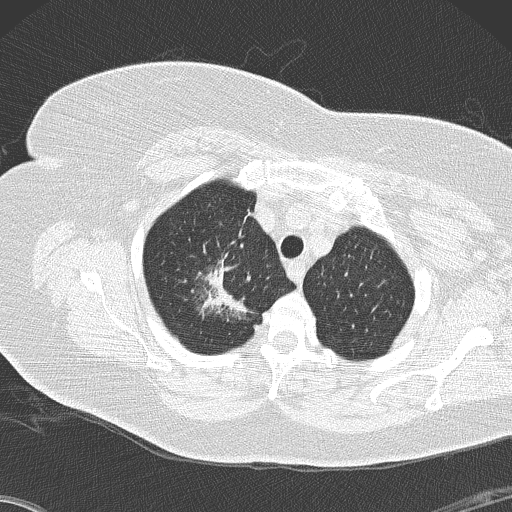
Axial slice from a low-dose chest CT screening exam, second screening round (one year after baseline), lung window (W 1500 / L -600 HU), 2 mm slice thickness, lung (sharp) reconstruction kernel (B50f), slice 25 of 146 in the series. Female, age 72 years at enrolment. Former smoker at enrolment.
- Expert reader's lesion annotation, bounding box <181,243,261,327> (left, top, right, bottom; pixels).
- The screening reader recorded 4 non-calcified nodules or masses ≥4 mm on this exam (right lower lobe, right lower lobe, right lower lobe, right upper lobe); which of them this box marks is not recorded.
- Official screen result: positive, other.
- Lung cancer was diagnosed 52 days after this screen: bronchiolo-alveolar adenocarcinoma, NOS, right upper lobe, stage IIIB (AJCC 6th edition), 45 mm at pathology.